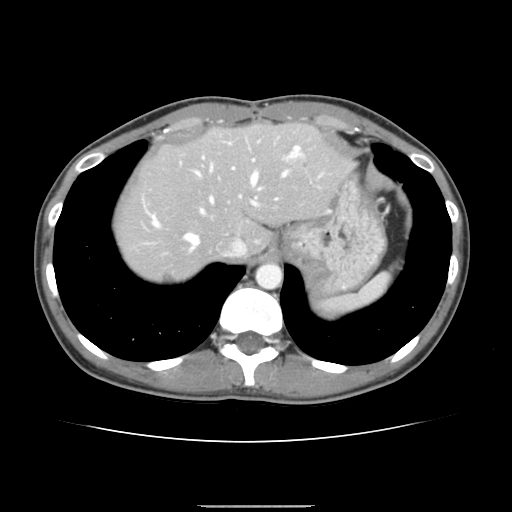
Contrast-enhanced abdominal CT, one axial slice. Slice 119 of 150 in the series (ordered by position). Intravenous contrast given. Soft-tissue window (W 400 / L 40 HU). 2.5 mm slice thickness. 512 × 512 image matrix, field of view 324 × 324 mm. Female patient, age 32 years. Case-level facts recorded for this patient, not image findings: diagnosis: colorectal cancer liver metastases, imaged before liver resection; multiple liver metastases: yes; largest metastasis: 0.7 cm; disease in both lobes: no.
Annotated regions visible in this slice (expert manual segmentation):
- hepatic veins: bounding box (x1, y1, x2, y2) in pixels: (151, 152, 294, 252)
- liver: (116, 124, 350, 282)
- planned liver remnant (the part of the liver to remain after resection): (116, 124, 351, 260)
- portal vein (with intrahepatic branches): (200, 146, 321, 214)
- liver metastasis: (163, 271, 174, 284)